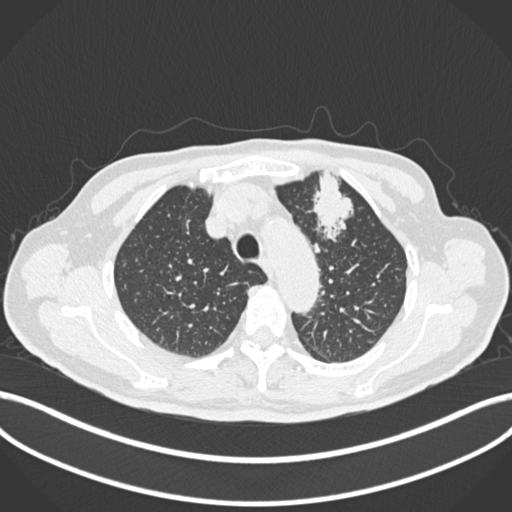
Chest CT, one axial slice; slice 201 of 261 in the series (ordered by position); 120 kVp; lung window (W 1500 / L -600 HU); 1 mm slice thickness; 512 × 512 image matrix, field of view 400 × 400 mm. Patient: male, 74 years. Case-level facts recorded for this patient, not image findings: clinical TNM (as recorded): T2b N0 M1c.
Outlined on this slice (bounding box drawn by a radiologist):
- lung tumour (recorded histology: adenocarcinoma): bounding box [x1, y1, x2, y2] px = [309, 169, 361, 247]